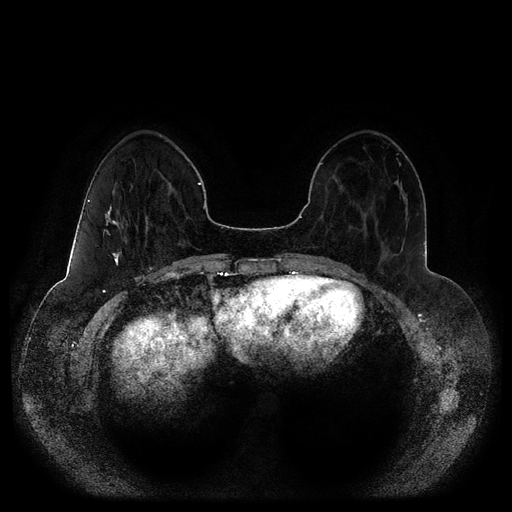
Breast MRI (dynamic contrast-enhanced, multi-phase), one axial slice. Slice 33 of 116 in the series (ordered by position). Dynamic contrast-enhanced series, time point 2 of 5 at this slice position (early post-contrast). 1.5 T. TE 2.5 ms, TR 5.2 ms. 2 mm slice thickness. 512 × 512 image matrix, field of view 390 × 390 mm. Patient: female, 44 years.
Structures marked on this image (semi-automatic segmentation, software-assisted and operator-edited):
- breast lesion (labelled 'tumour' in the annotation; benign lesions carry a separate 'benign' label): box from (x=103, y=204) to (x=123, y=266) px